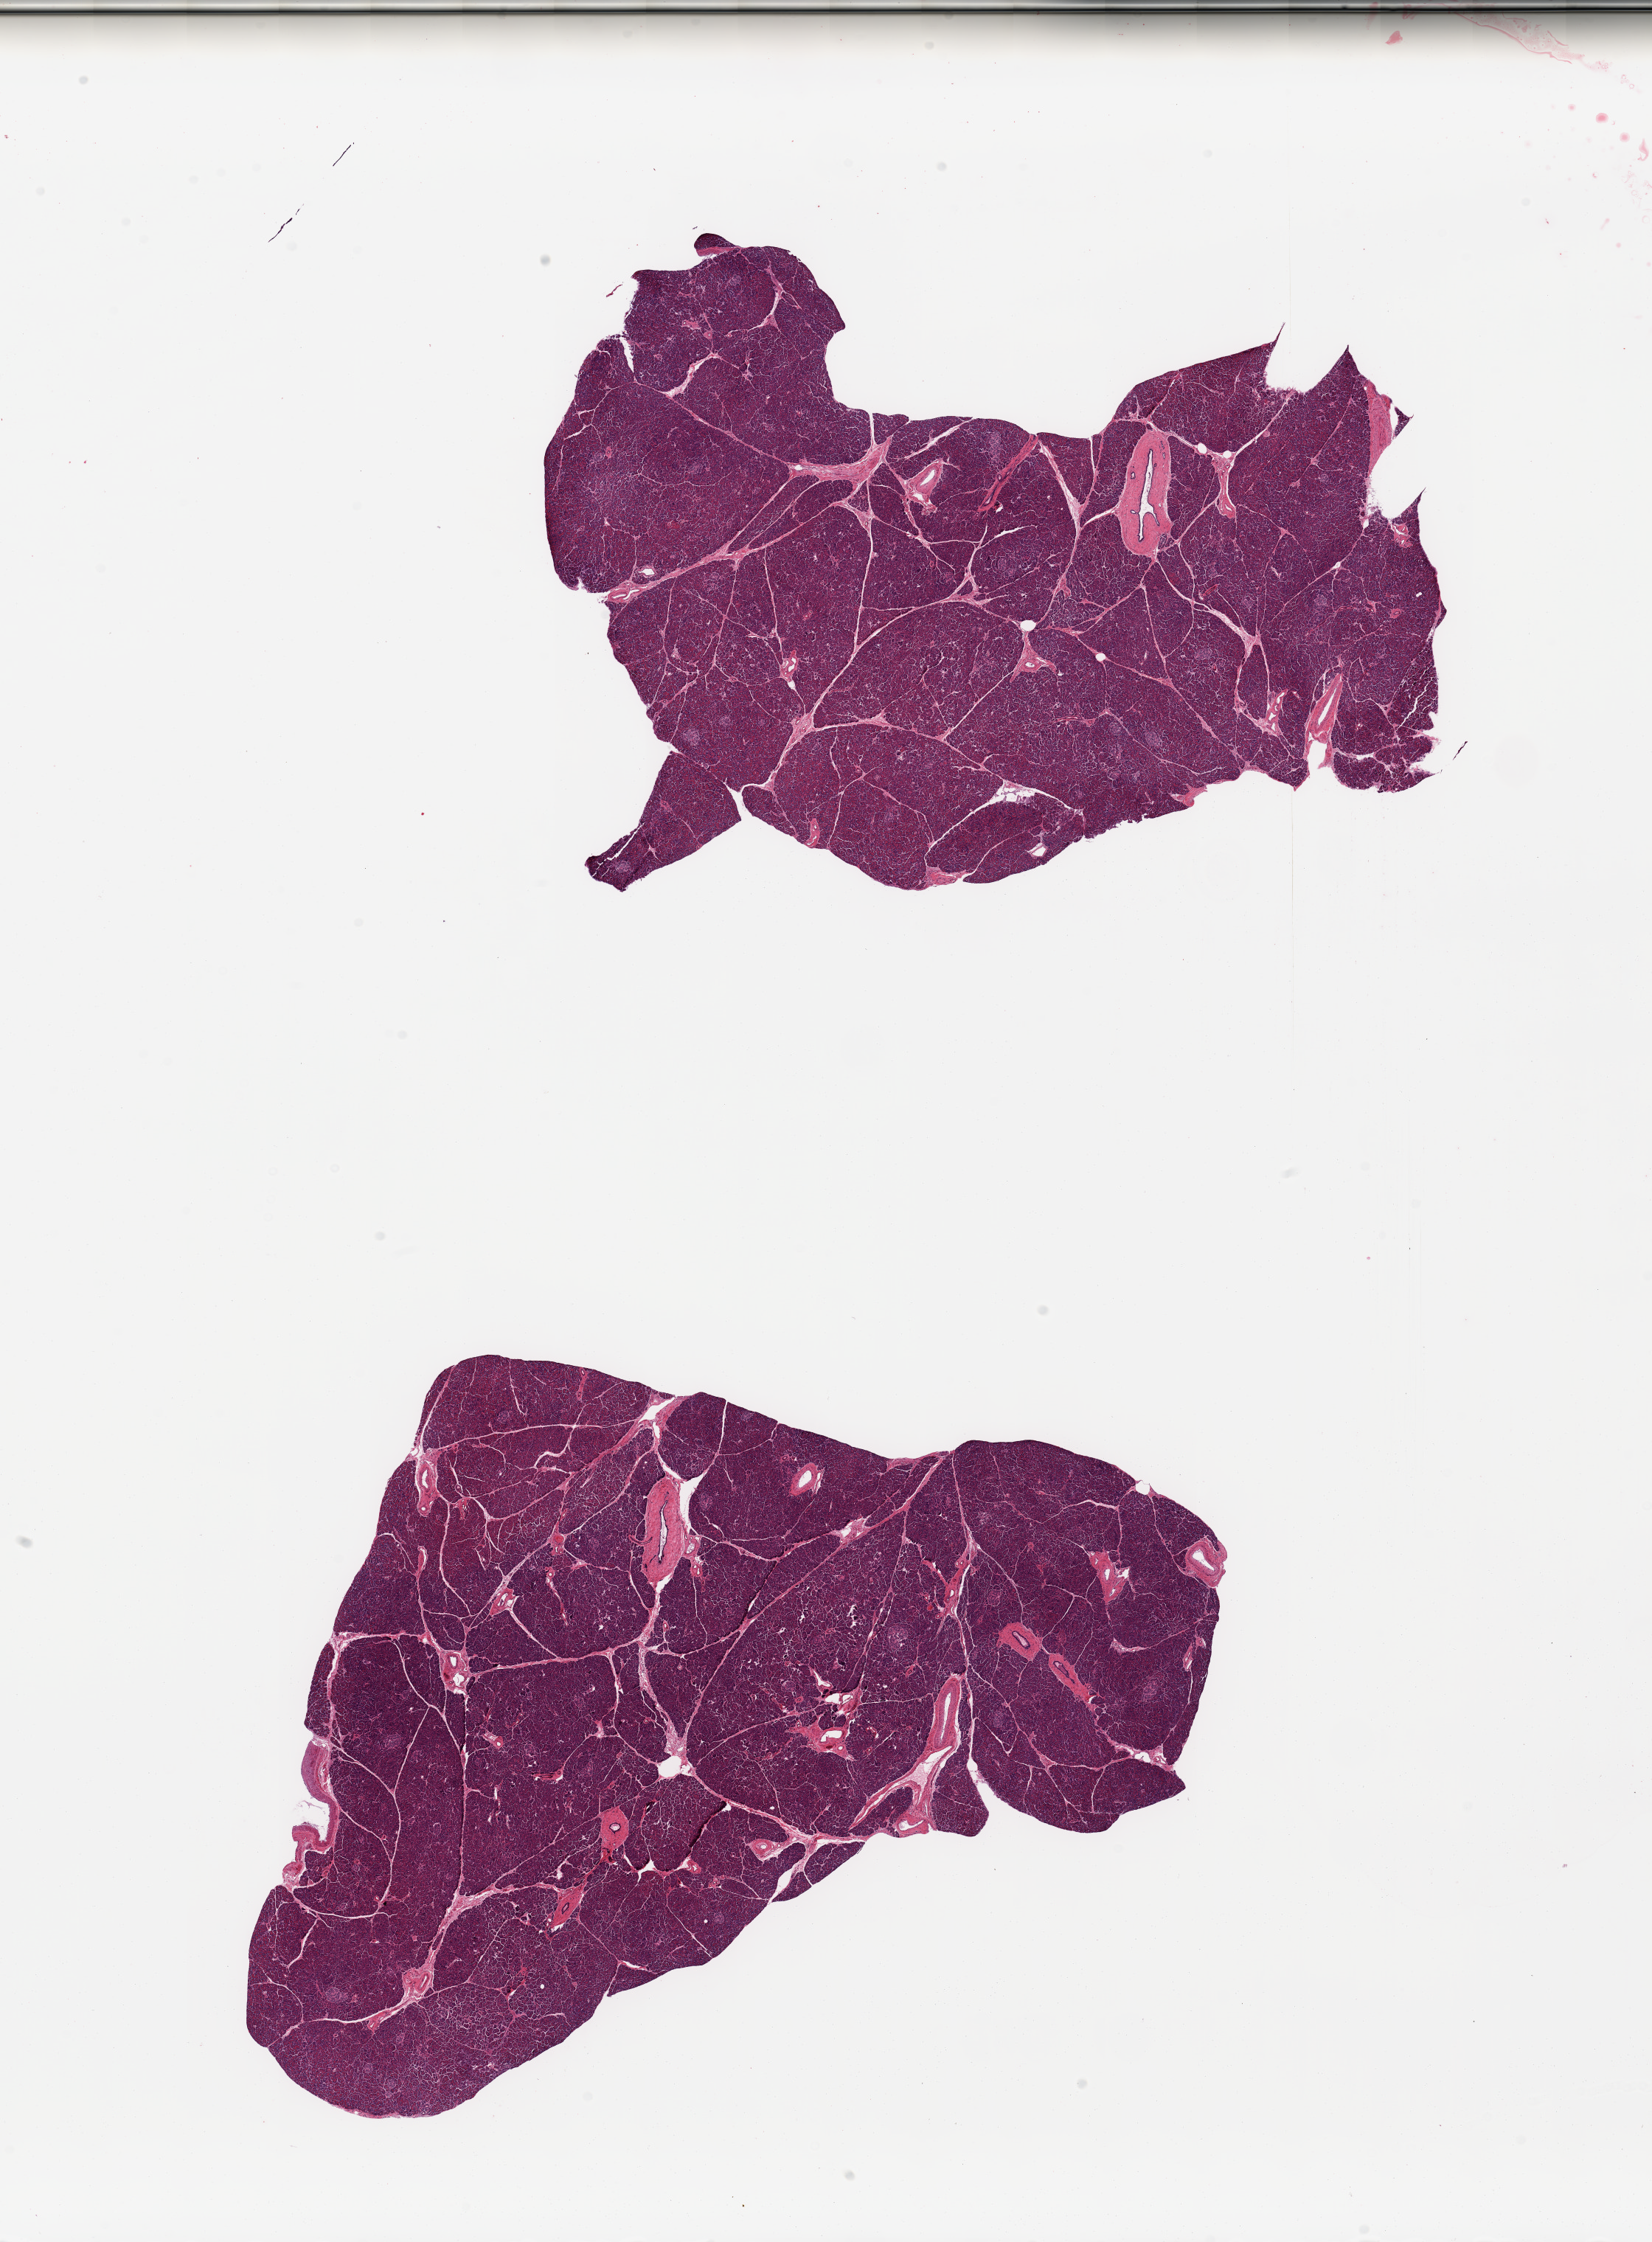
Whole-slide image, haematoxylin and eosin stain — low-resolution overview of the scanned area, about 17.7 x 24.0 mm. PAXgene-fixed, paraffin-embedded tissue. Target tissue: pancreas. Tissue donor sample. Donor sex: male.
Reviewer comment on this tissue sample: 2 pieces, islets present but rare, well-preserved.